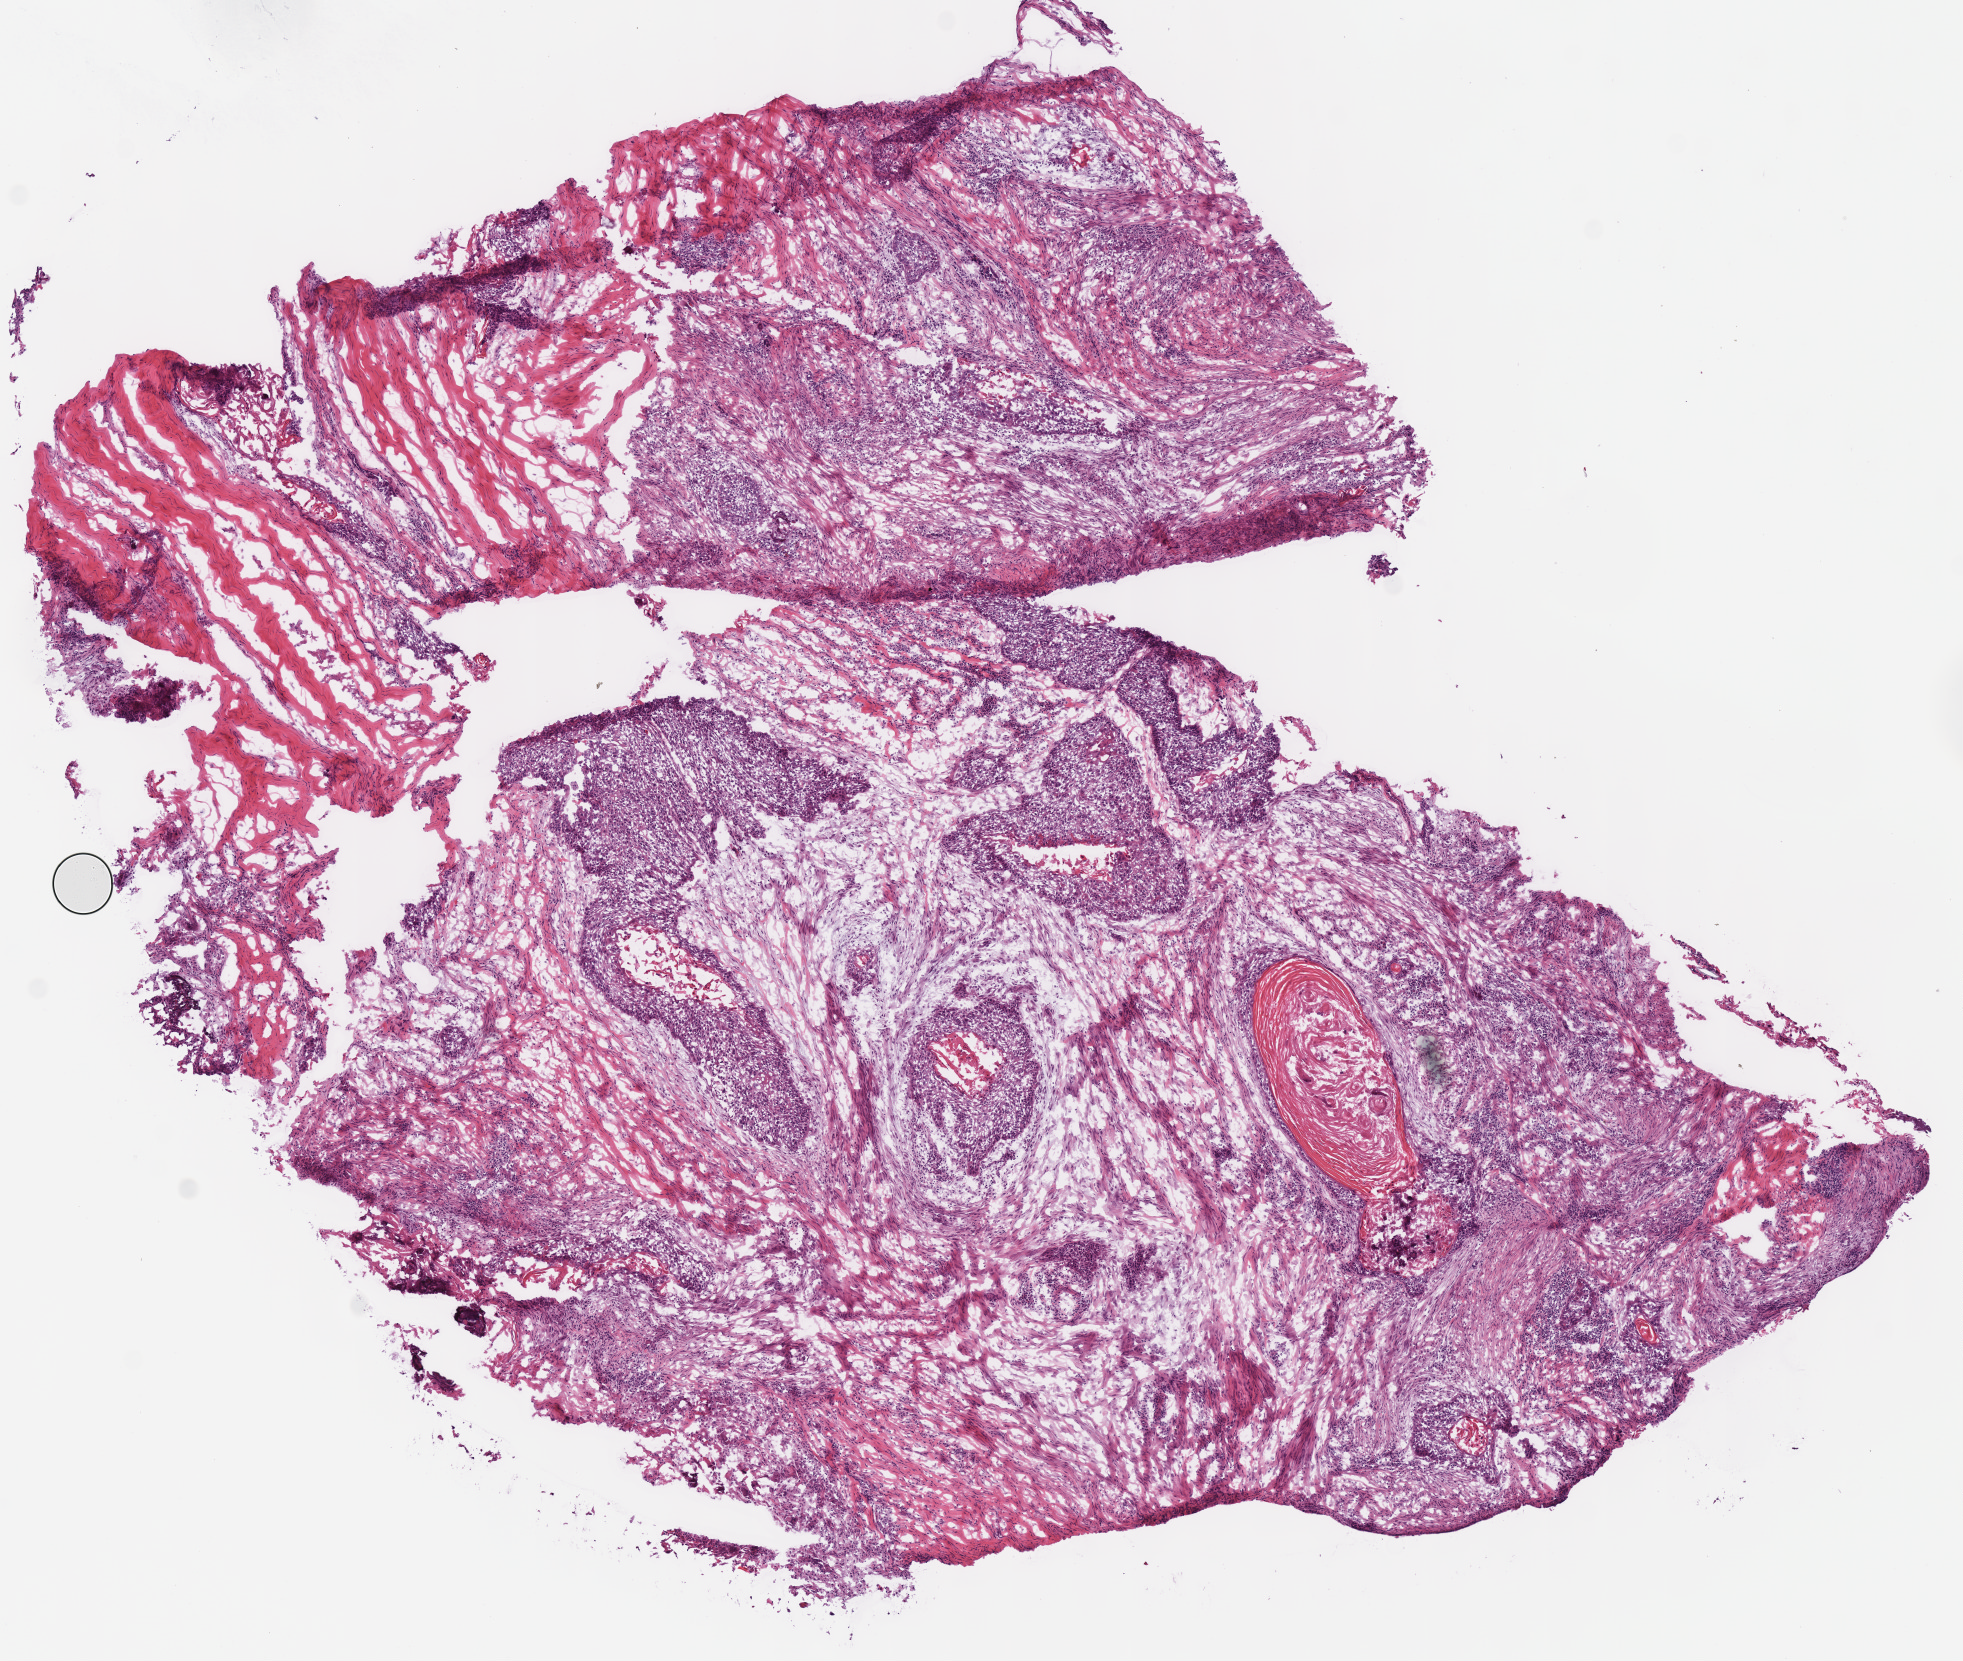
Digitized H&E-stained tissue section (whole slide), low-resolution overview of the scanned area, about 7.7 x 6.5 mm (slide scanned at 40x). Frozen section. Sample: primary tumour, head and neck. Female patient; age at initial diagnosis 57 years. Histologic grade: G2 (moderately differentiated). Pathologist review of this section (percent, as recorded): tumour cells 50%, tumour nuclei 60%, normal cells 0%, stromal cells 50%, necrosis 0%.
- AJCC pathologic stage: IVA (7th edition)
- pathologic diagnosis: Squamous cell carcinoma, NOS (overlapping lesion of lip, oral cavity and pharynx)